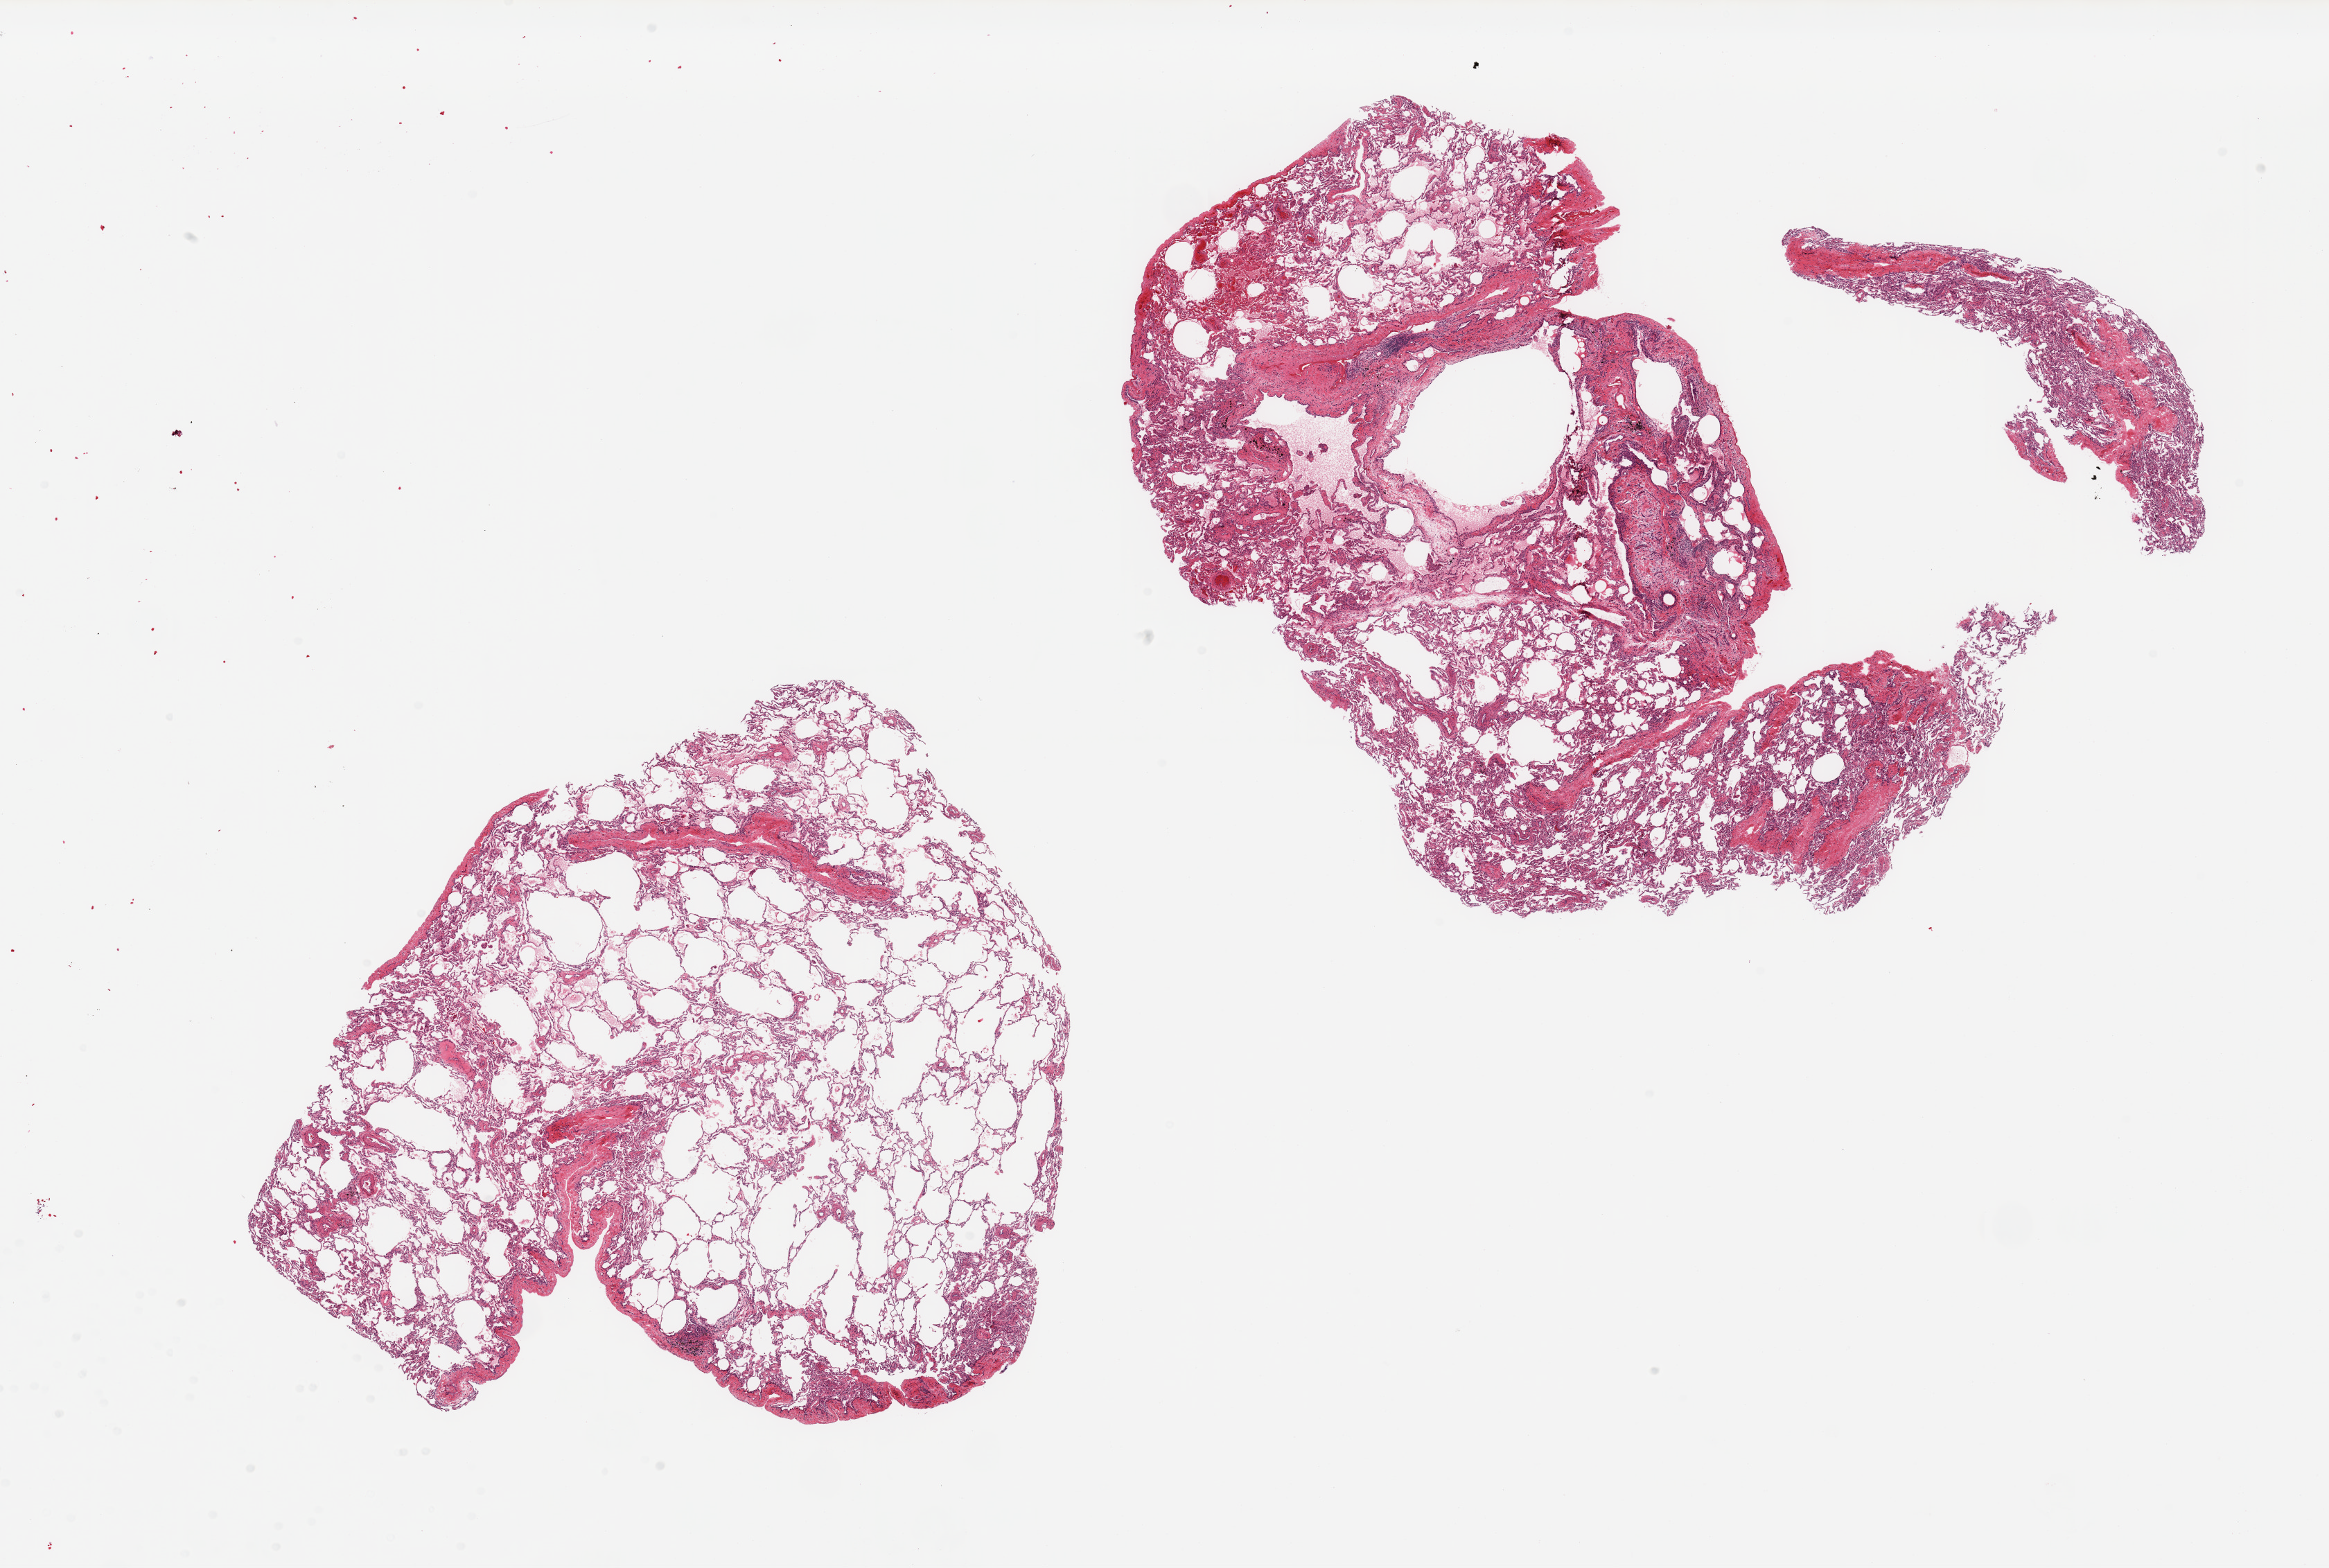
Haematoxylin and eosin whole-slide image, low-resolution overview of the scanned area, about 26.6 x 17.9 mm, PAXgene-fixed, paraffin-embedded tissue, sampled site (target tissue): lung, tissue donor sample. Male donor.
Review note (as recorded): 2 pieces, pronounced emphysematous changes.